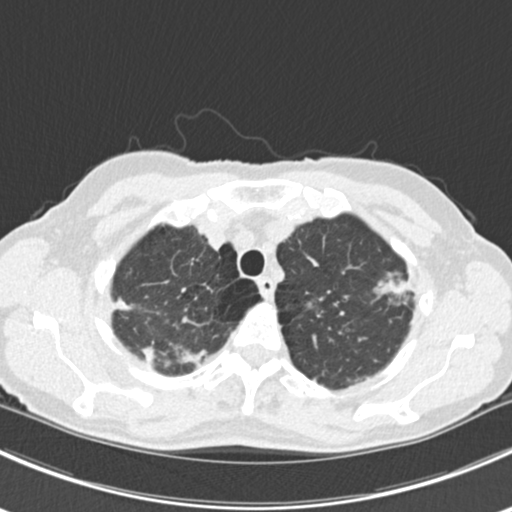
Chest CT (low-dose screening protocol), one axial image. Baseline screening round. Lung window (W 1500 / L -600 HU). Standard (soft-tissue) reconstruction kernel (B30f). Slice 34 of 224 in the series. 512 × 512 image matrix, field of view 310 × 310 mm. Female, age 63 years at enrolment.
Expert reader's lesion annotation, bounding box (x1, y1, x2, y2) in pixels: (366, 261, 422, 318). The screening reader recorded 10 non-calcified nodules or masses ≥4 mm on this exam (right lower lobe, right lower lobe, left lower lobe, left lower lobe, right middle lobe, right lower lobe, left lower lobe, left upper lobe, right upper lobe, left upper lobe); which of them this box marks is not recorded. Official screen result: positive, change unspecified: nodule(s) >= 4 mm or enlarging nodule(s), mass(es), or other non-specific abnormalities suspicious for lung cancer.